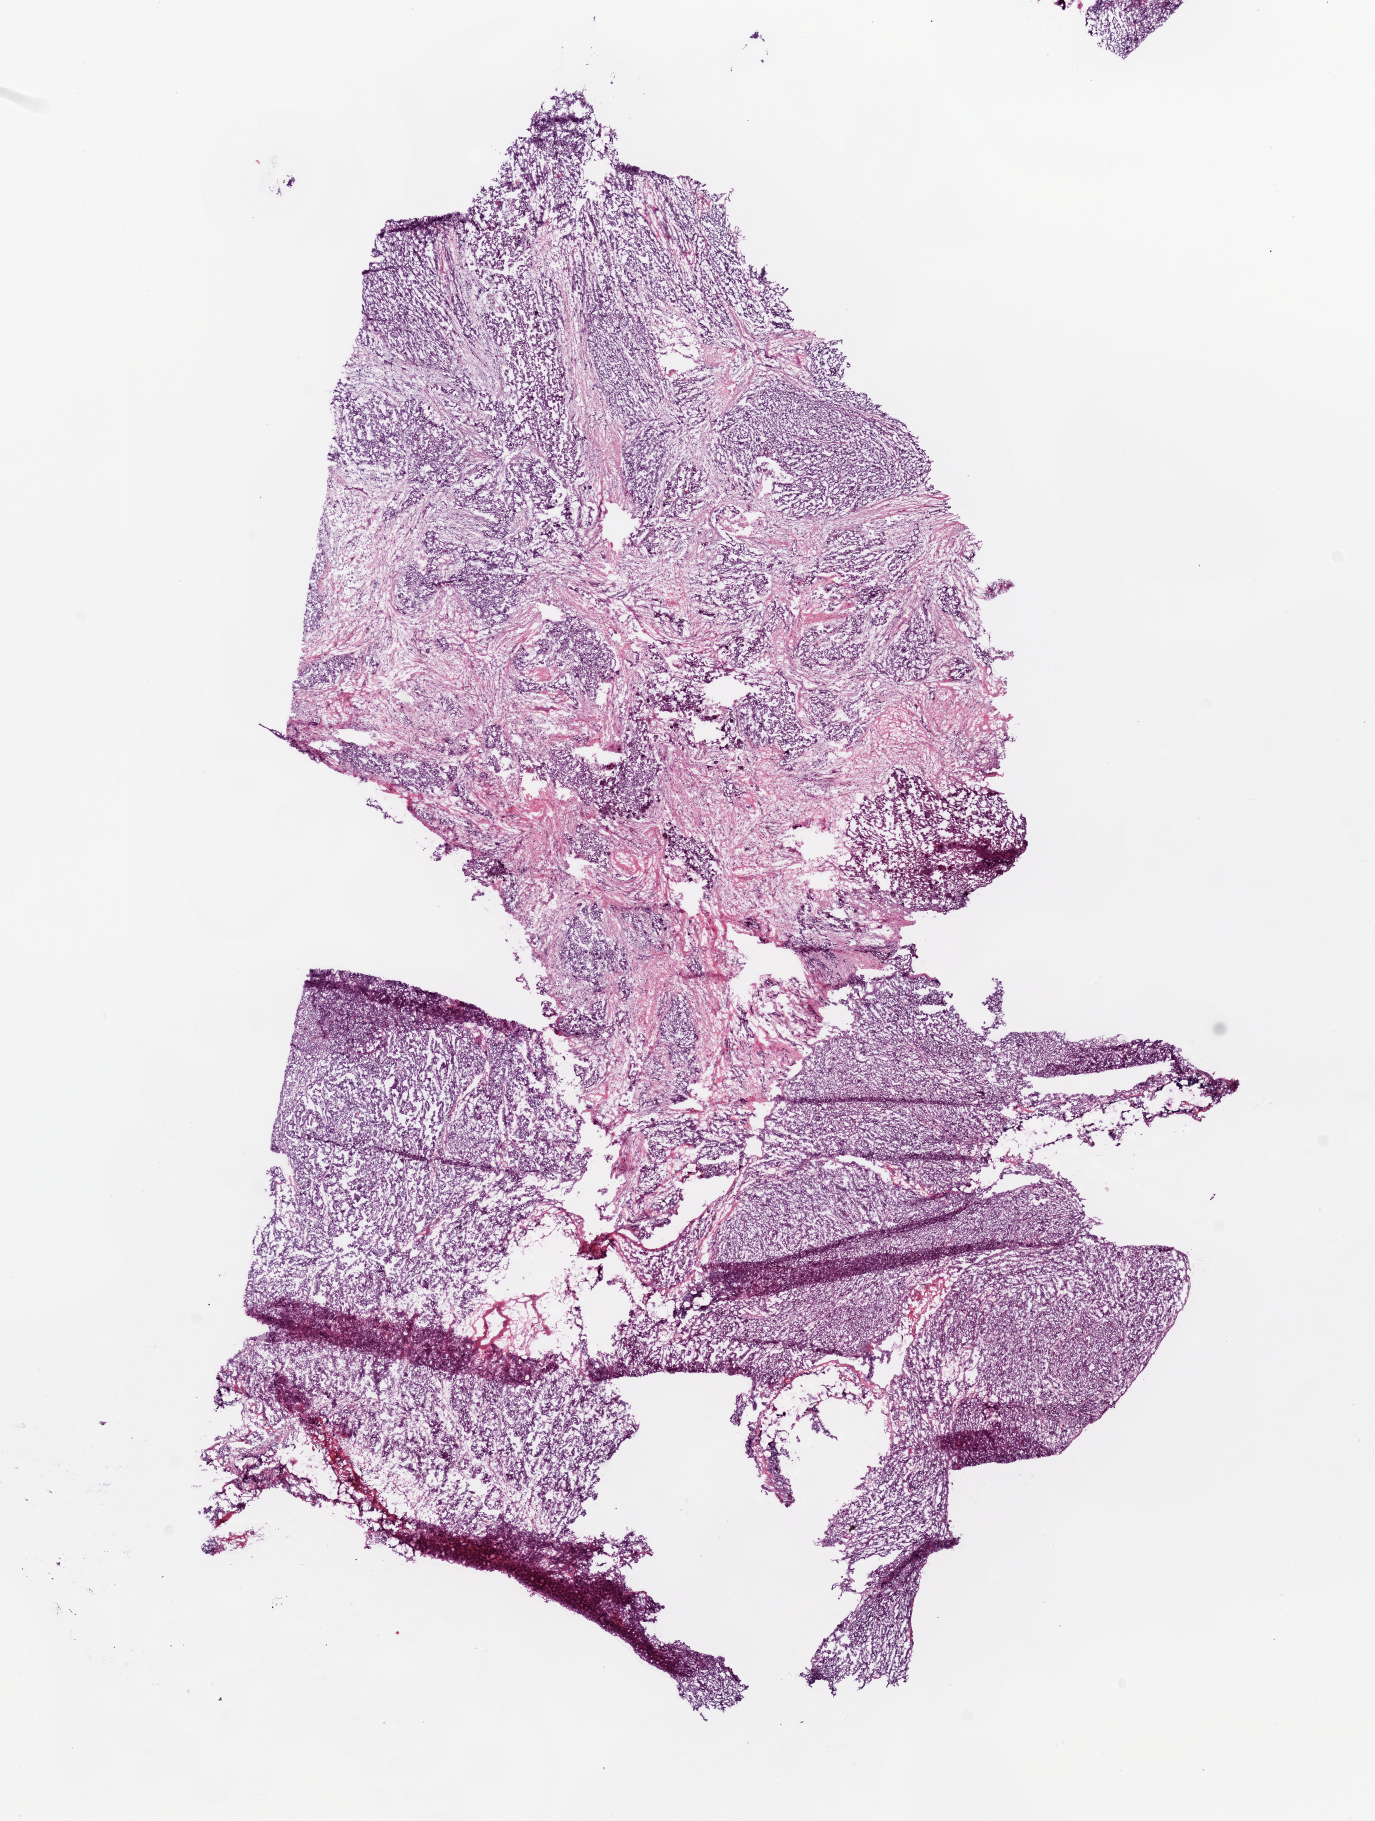
Whole-slide histology image, H&E — low-resolution overview of the scanned area, about 11.0 x 14.6 mm; frozen section from the top of the tissue portion; ovary, primary tumour sample. Female, age 55 years at initial diagnosis. Histologic grade: G3 (poorly differentiated). Composition of this section per pathologist review: tumour cells 80%, tumour nuclei 80%, normal cells 0%, stromal cells 20%, necrosis 0%.
- FIGO stage: IIIC
- histologic diagnosis: Serous cystadenocarcinoma, NOS